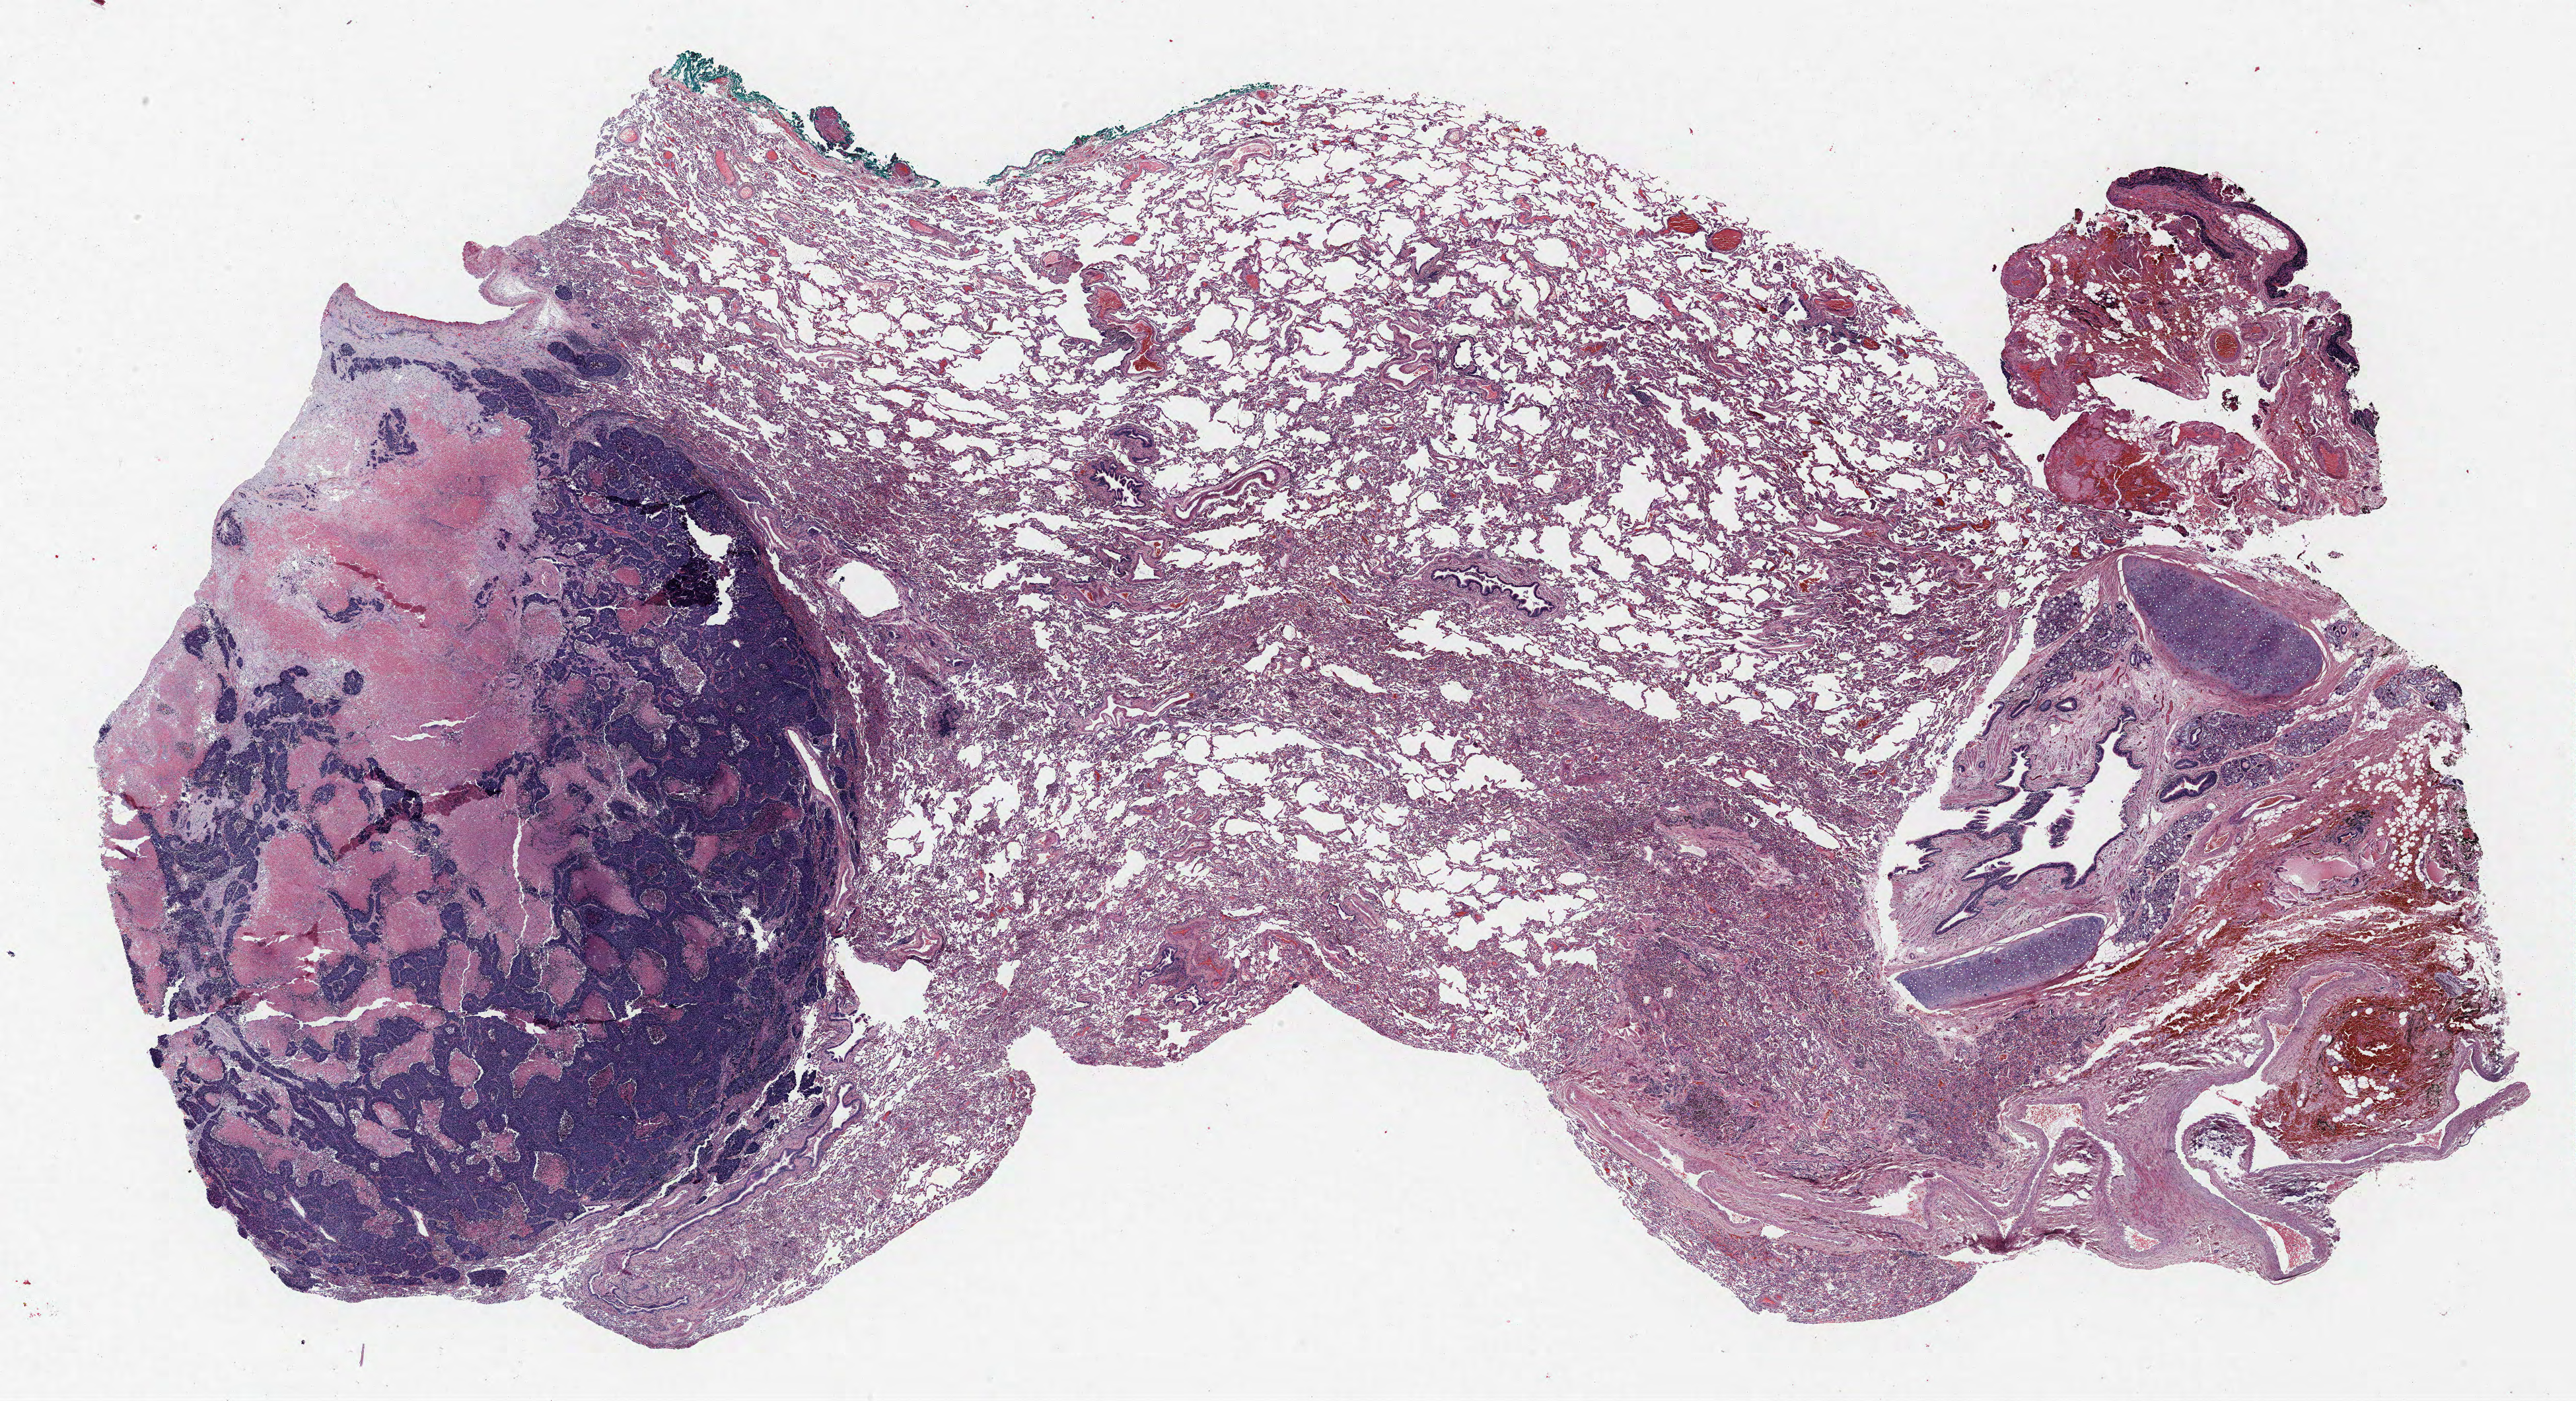
Whole-slide histology image, H&E-stained, shown as a low-resolution overview of the whole scanned area (about 31.2 x 17.0 mm, acquisition: 40x scan), formalin-fixed paraffin-embedded (FFPE) section, lung. Male, age 60 at enrolment. Current smoker at enrolment. Grade: poorly differentiated (G3).
* primary tumour location (clinical record): left lower lobe
* participant's lung-cancer diagnosis: Large cell neuroendocrine carcinoma
* stage (AJCC 6th edition): IB
* ICD-O-3 topography: lower lobe of lung (C34.3)
* tumour size (pathology): 33 mm